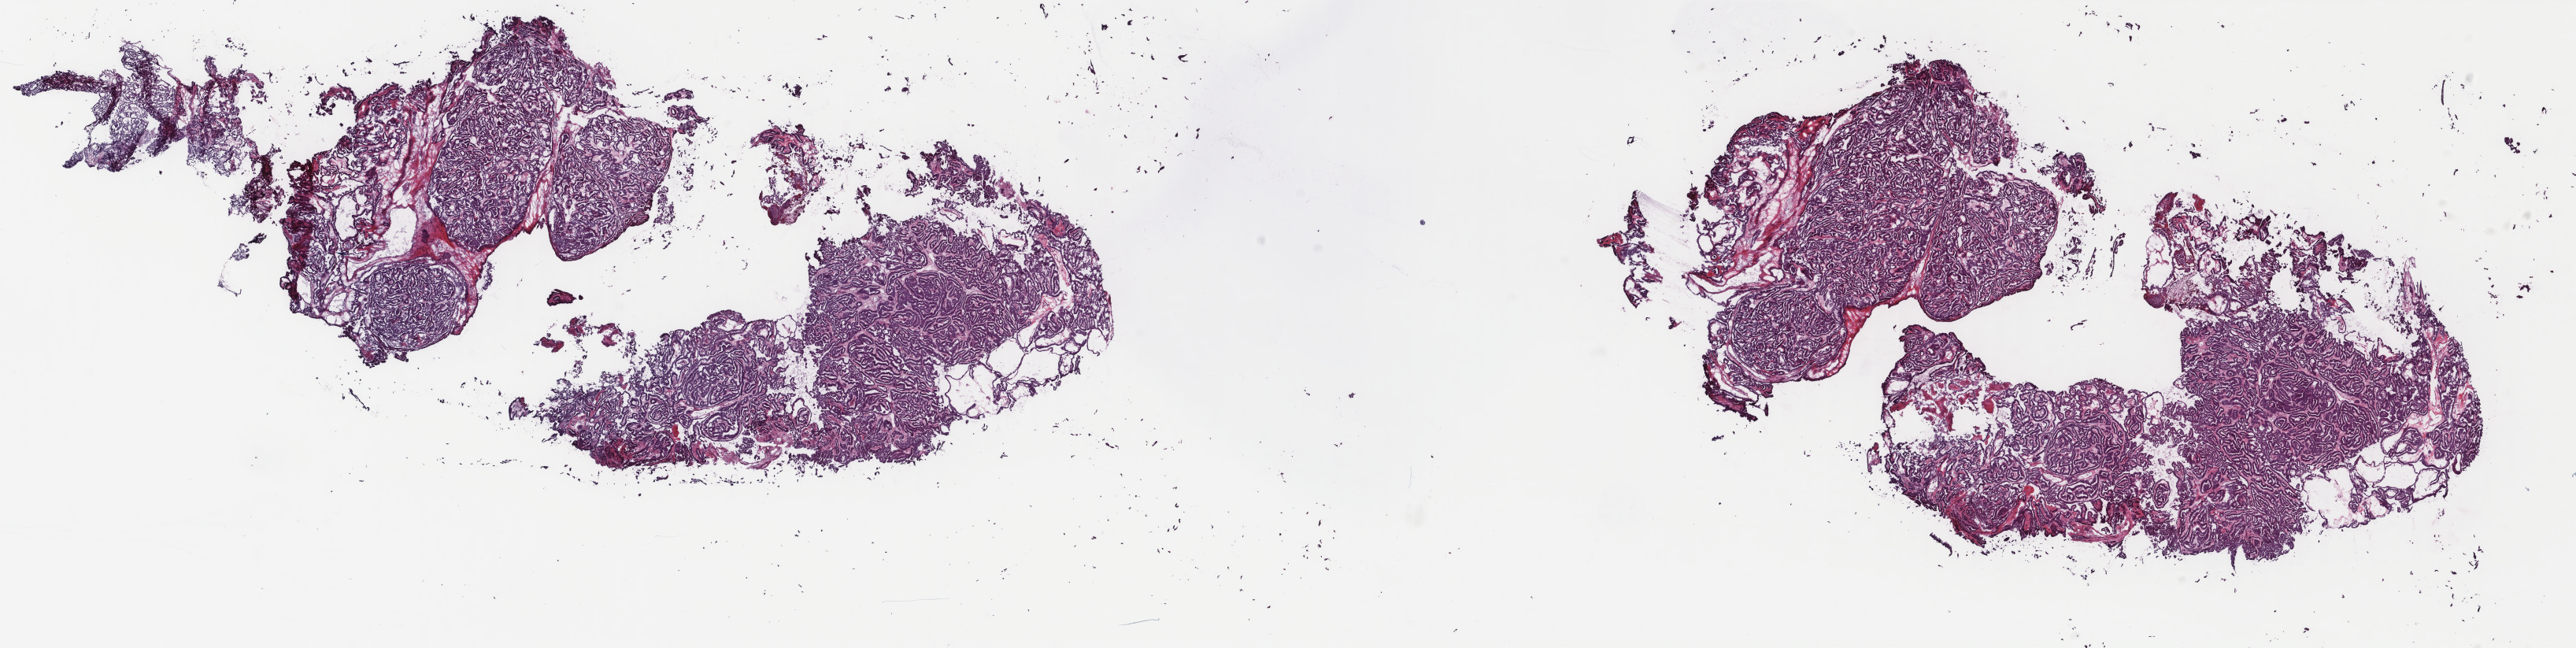
Digitized H&E-stained tissue section (whole slide), whole scanned area (about 26.0 x 6.5 mm) shown as a low-resolution overview; frozen section from the top of the tissue portion; thyroid, primary tumour sample. Patient: female, age at initial diagnosis 33 years. Slide review estimates, as recorded: tumour cells 90%, tumour nuclei 100%, normal cells 0%, stromal cells 10%, necrosis 0%. Inflammatory infiltration, as recorded: lymphocyte infiltration 1%, monocyte infiltration 2%, neutrophil infiltration 0%.
* laterality: left
* lymph nodes positive (case pathology): 12 of 19 examined
* diagnosis: Papillary adenocarcinoma, NOS
* AJCC pathologic stage: I